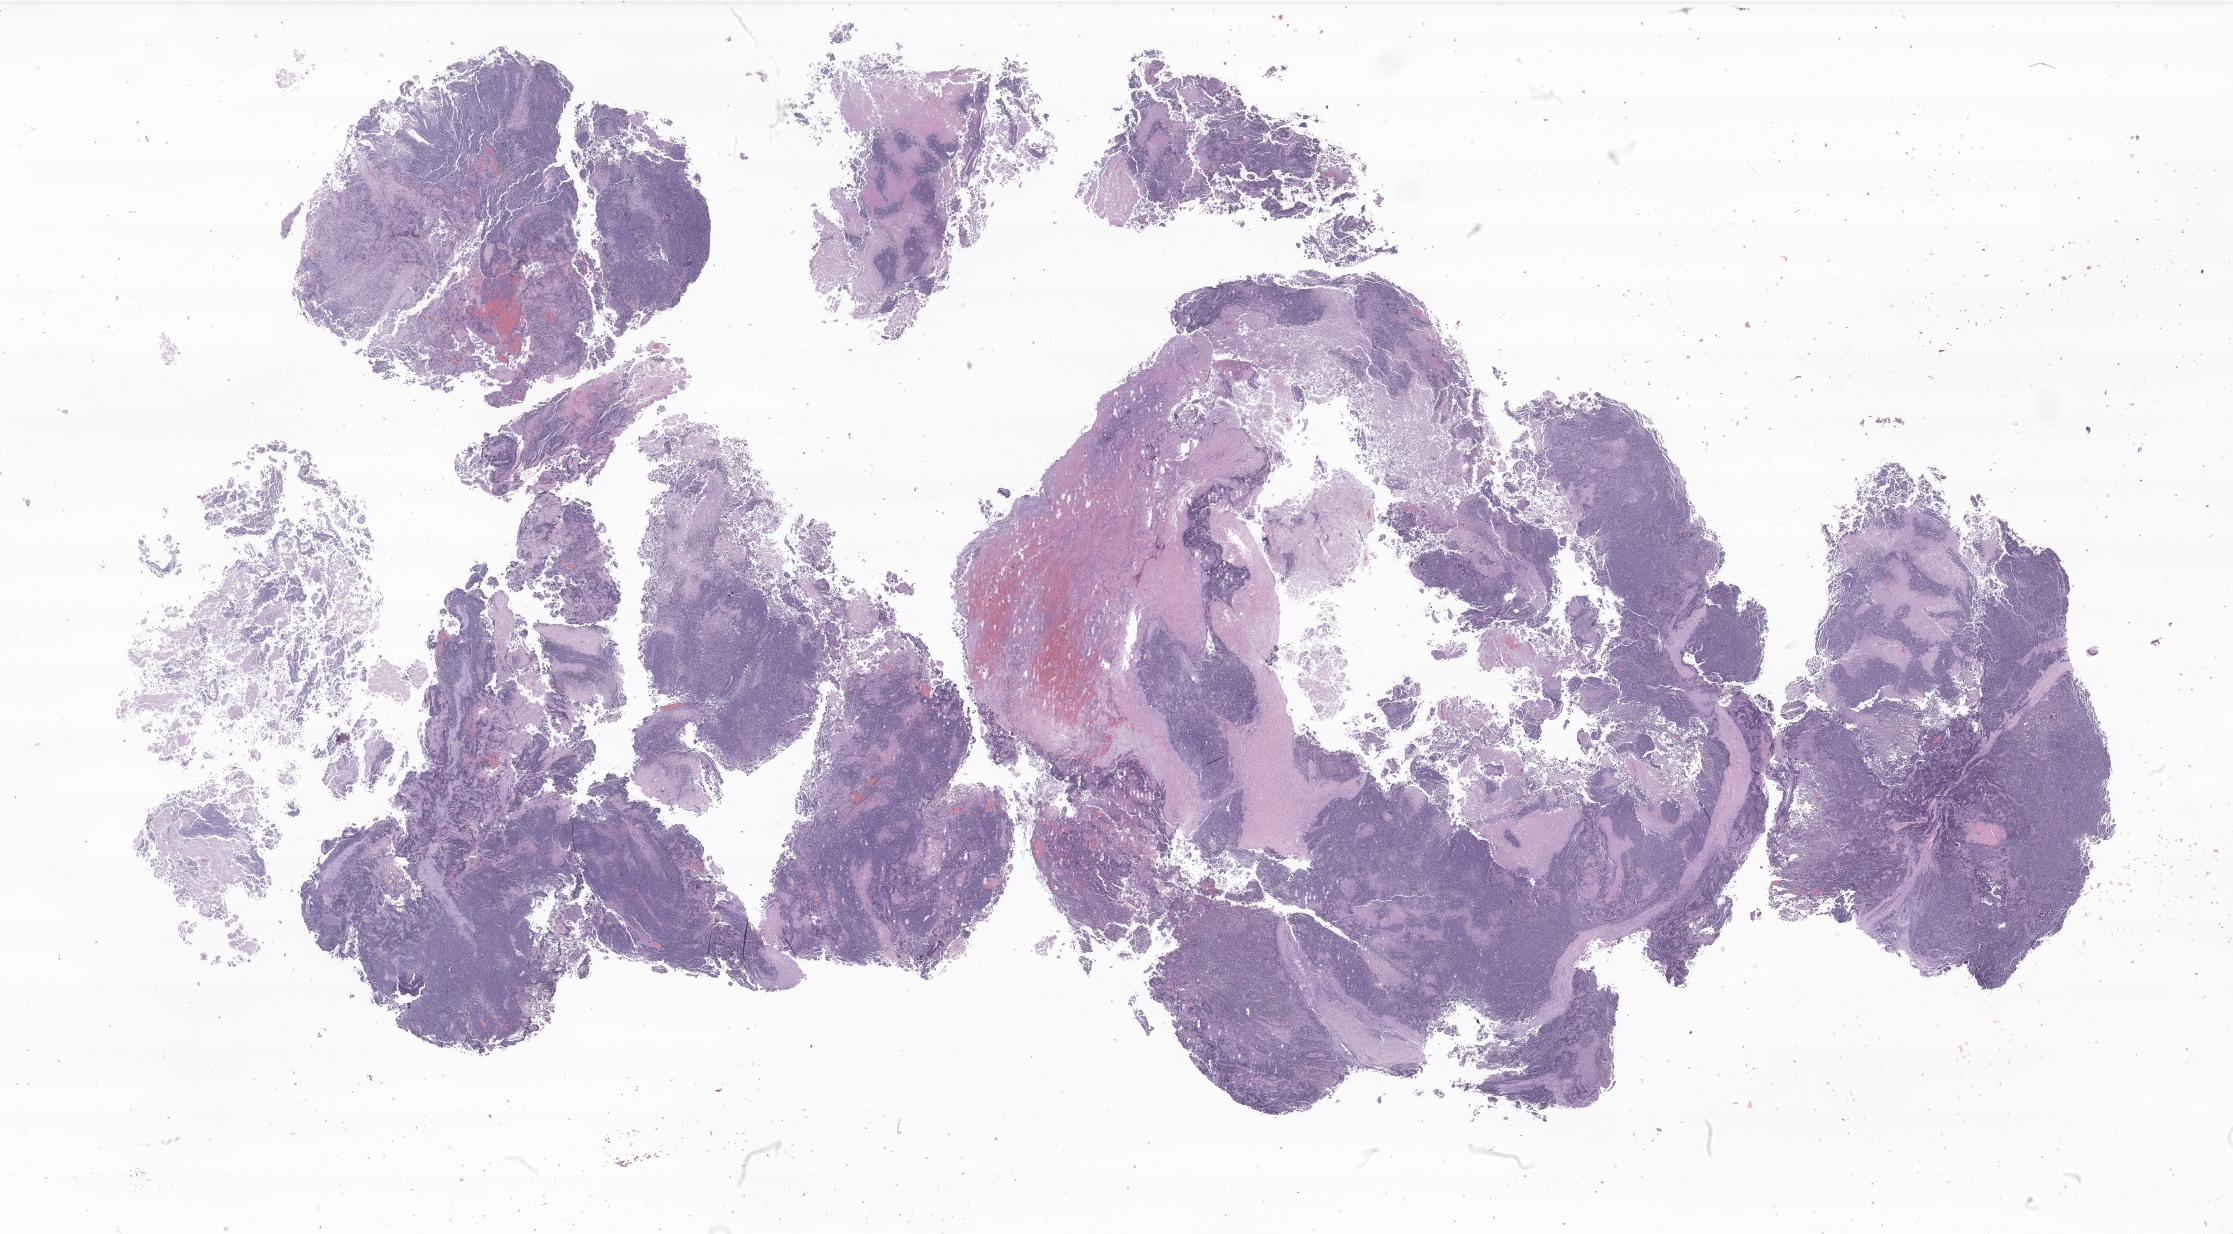
Hematoxylin and eosin (H&E) whole-slide image of tumor tissue from the soft tissue of lower extremity — a low-resolution overview of the entire scanned area, about 37.7 x 20.8 mm, formalin-fixed paraffin-embedded section. Male patient, age 144 months (12 years).
- tissue or organ of origin (case record): connective, subcutaneous and other soft tissues of lower limb and hip
- diagnosis: Rhabdomyosarcoma, NOS